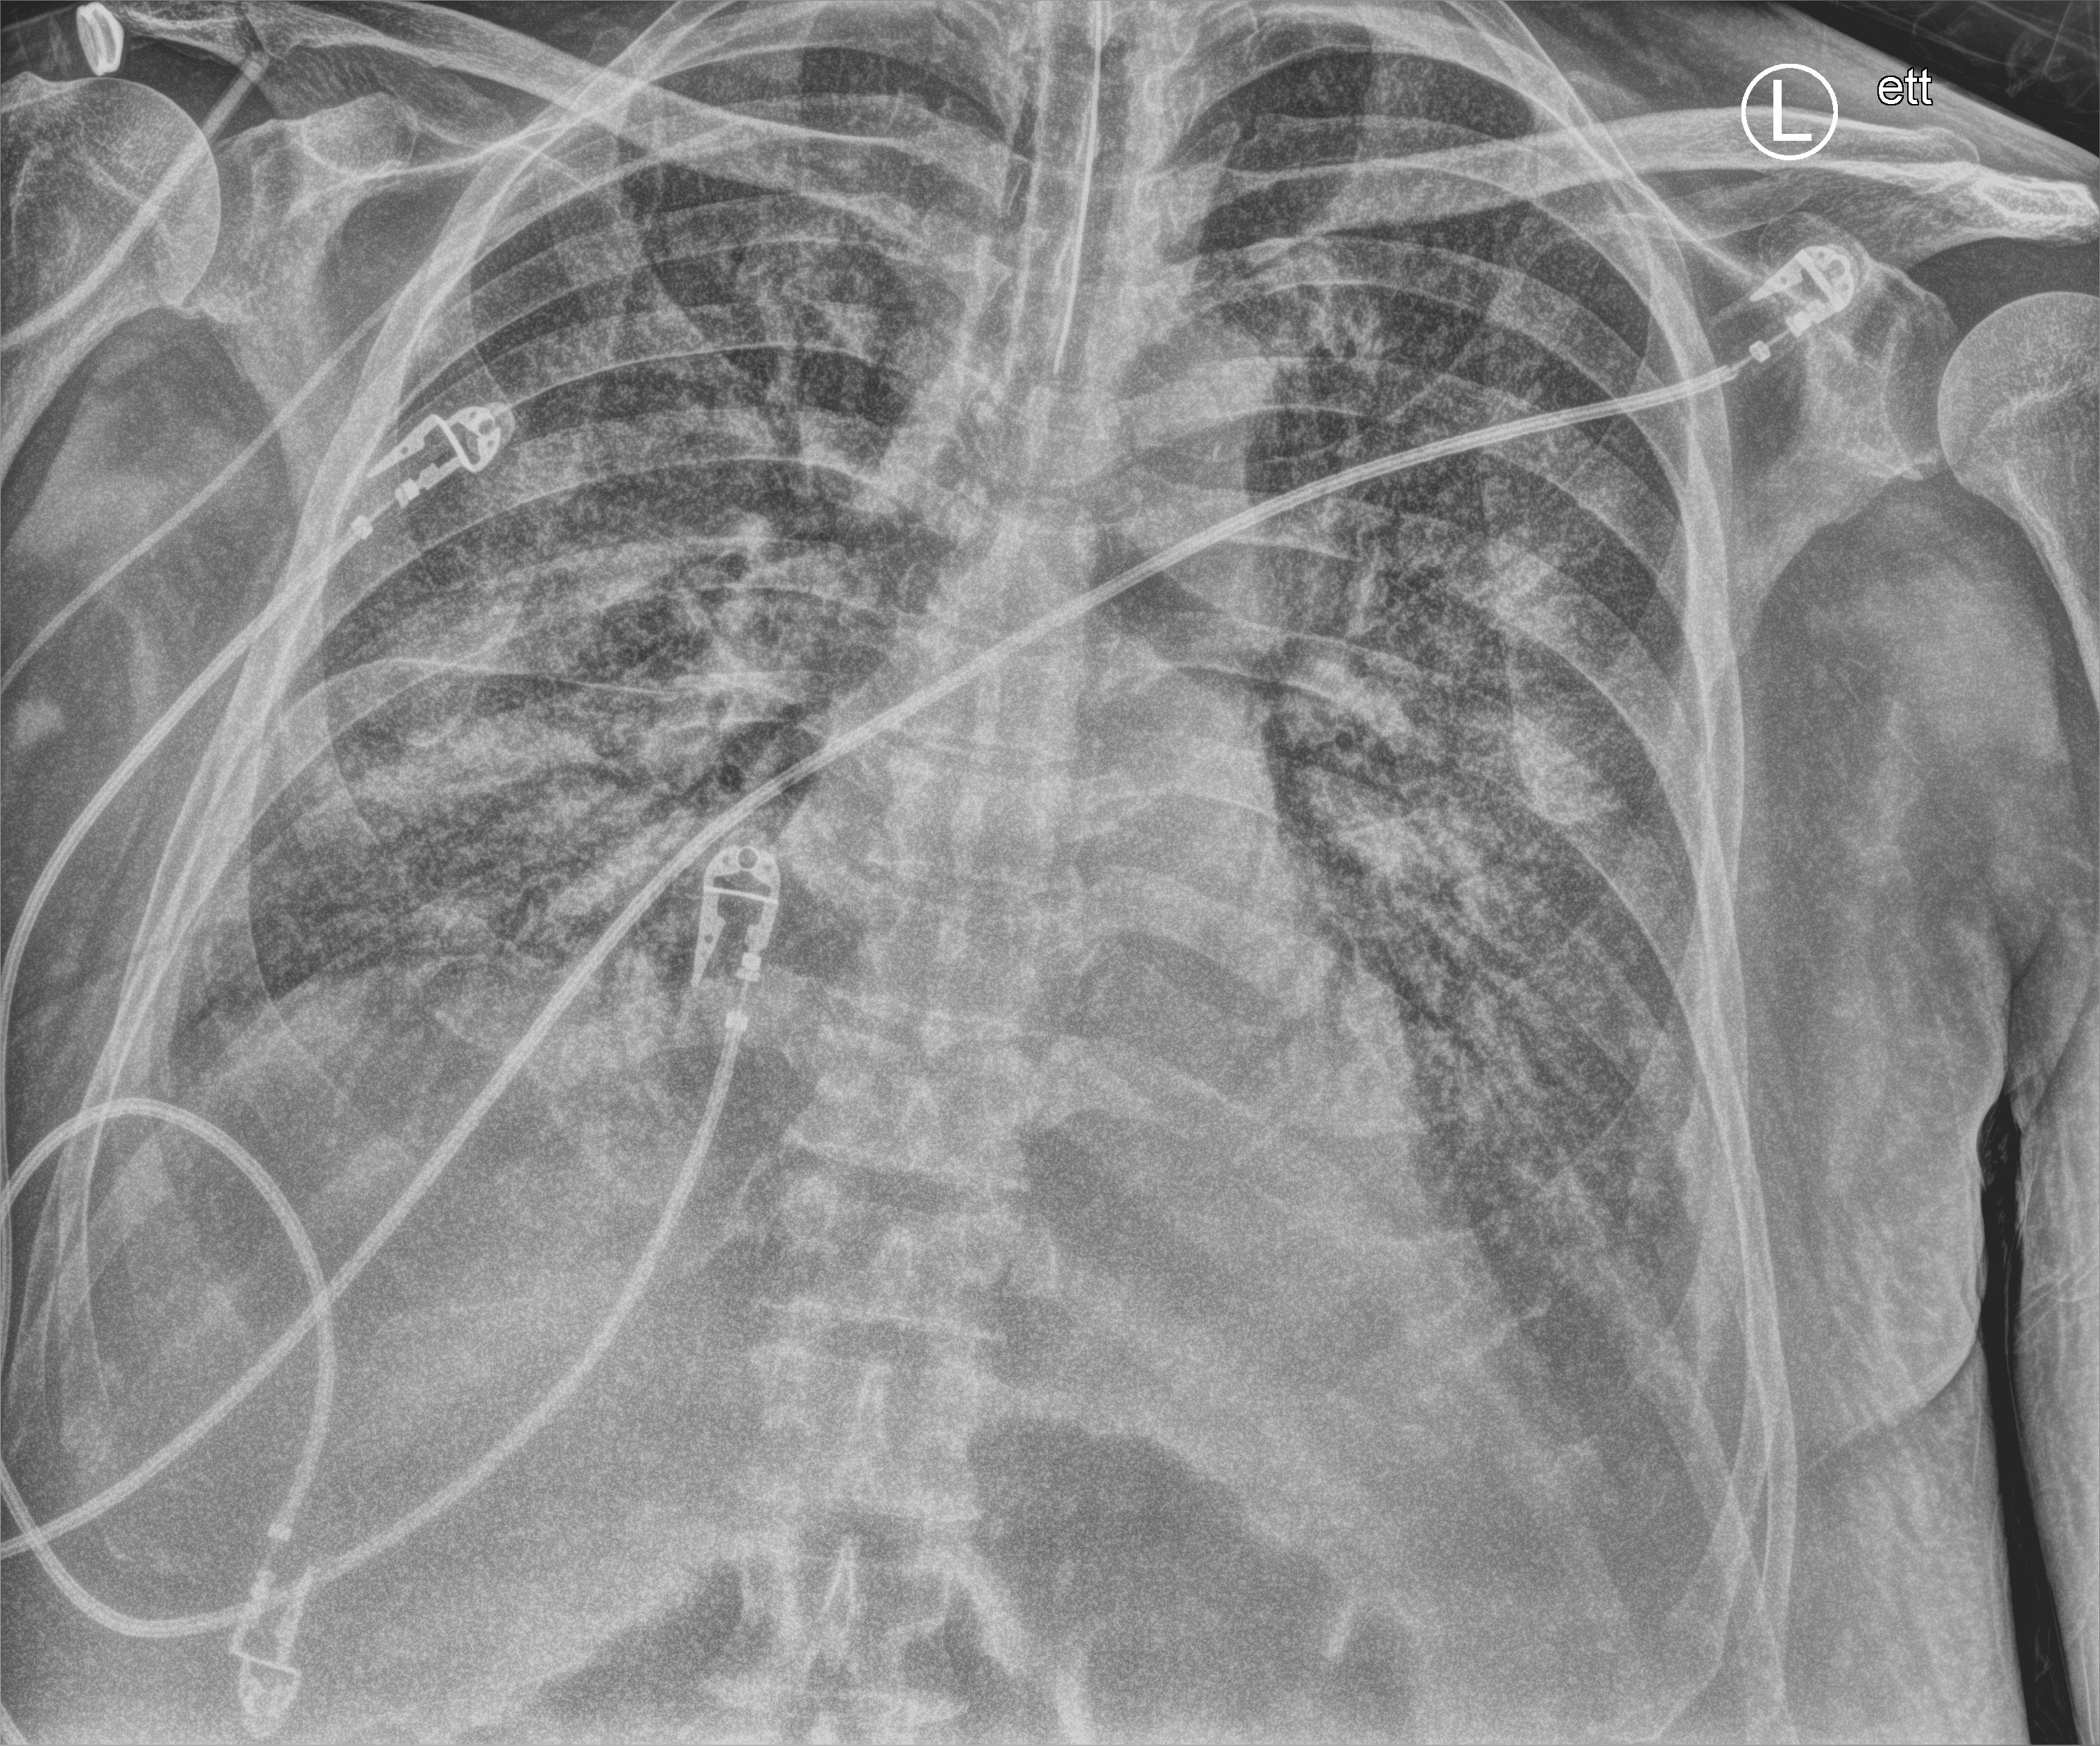
Bedside chest radiograph (computed radiography), anteroposterior (AP) projection. Patient hospitalised with COVID-19; male, aged 60–74 years.
Hospital-stay facts (about this admission, not read from this image; timing relative to this image not recorded): admitted to intensive care during this hospital stay: yes.